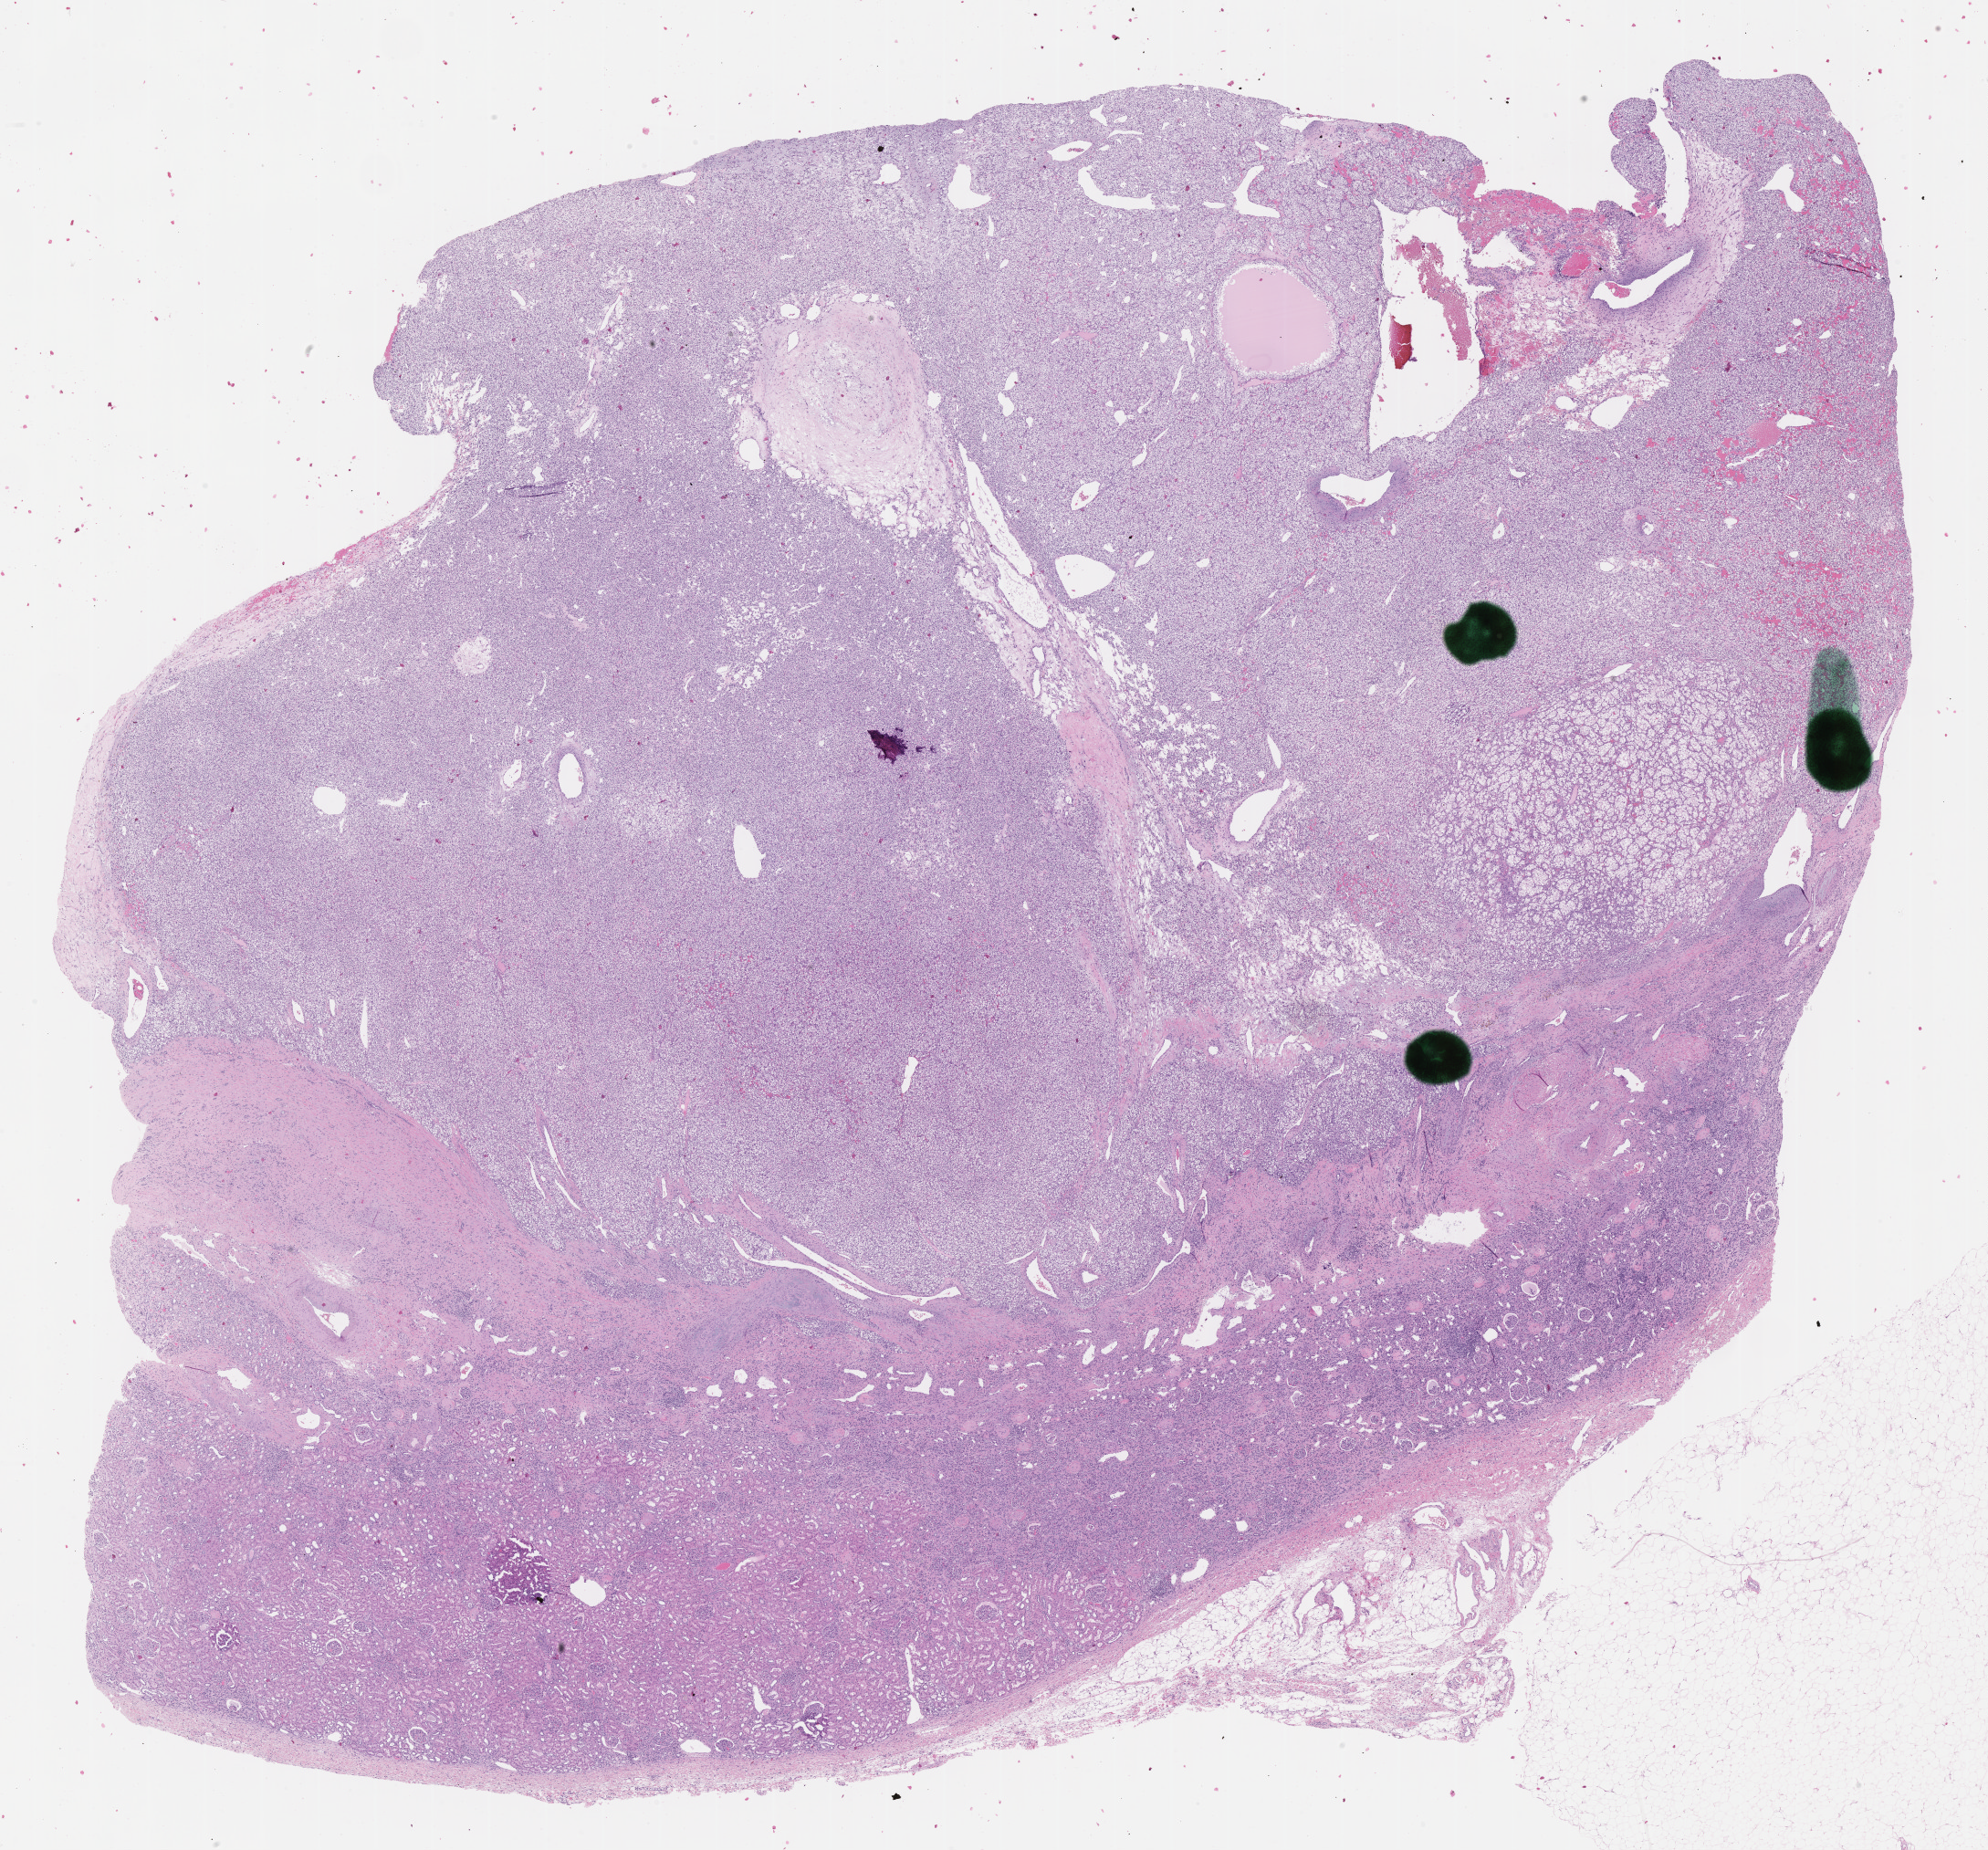
Hematoxylin and eosin (H&E) stained whole-slide image — a low-resolution overview of the entire scanned area, about 17.6 x 16.4 mm; FFPE section; kidney, primary tumour sample. Female patient; age at initial diagnosis 62 years. Histologic grade: G2 (moderately differentiated).
* AJCC pathologic stage: I
* laterality: right
* TNM: T1a NX M0
* diagnosis: Clear cell adenocarcinoma, NOS